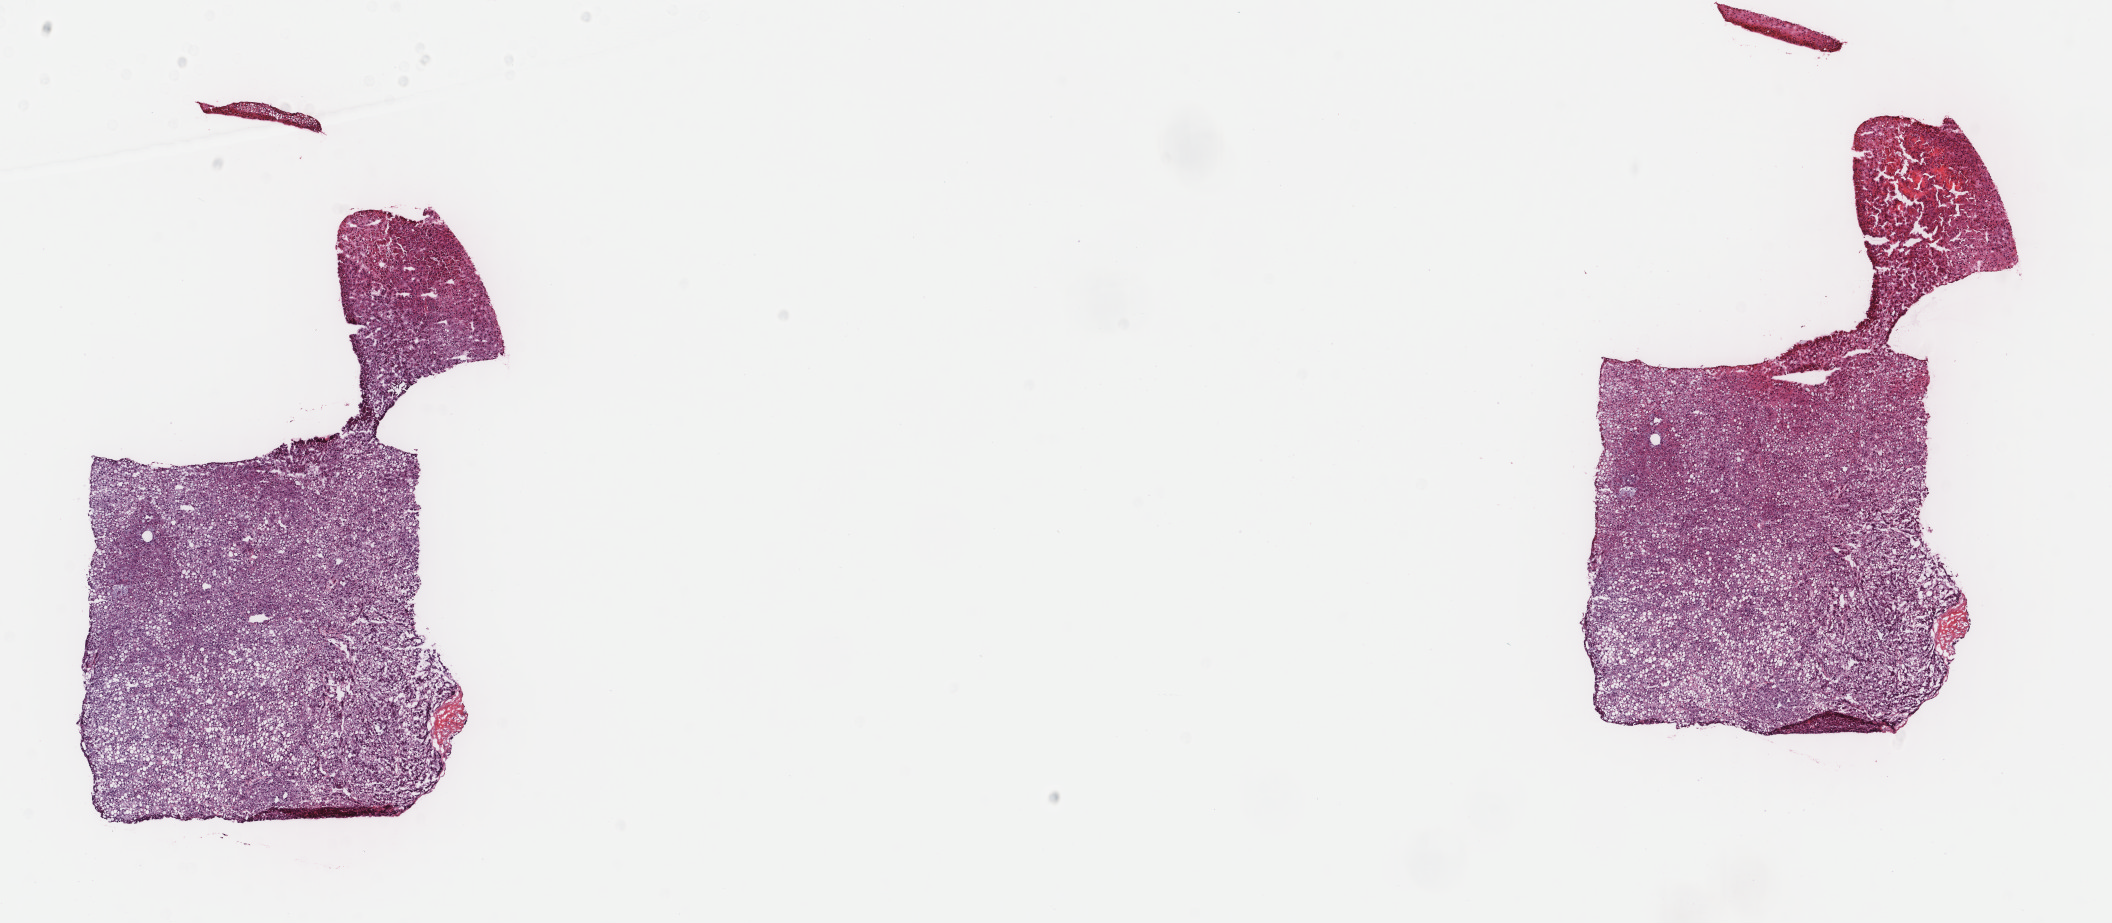
Digitized H&E-stained tissue section (whole slide), low-resolution overview of the scanned area, about 16.8 x 7.3 mm (acquisition: 40x scan). Frozen section. Primary tumour sample from the liver. Male patient; age at initial diagnosis 62 years. Histologic grade: G3 (poorly differentiated). Pathologist review of this section (percent, as recorded): tumour cells 100%, tumour nuclei 98%, normal cells 0%, stromal cells 0%, necrosis 0%. Inflammatory infiltration, as recorded: lymphocyte infiltration 0%, monocyte infiltration 0%, neutrophil infiltration 0%.
AJCC pathologic stage: I. Histologic diagnosis: Hepatocellular carcinoma, NOS.